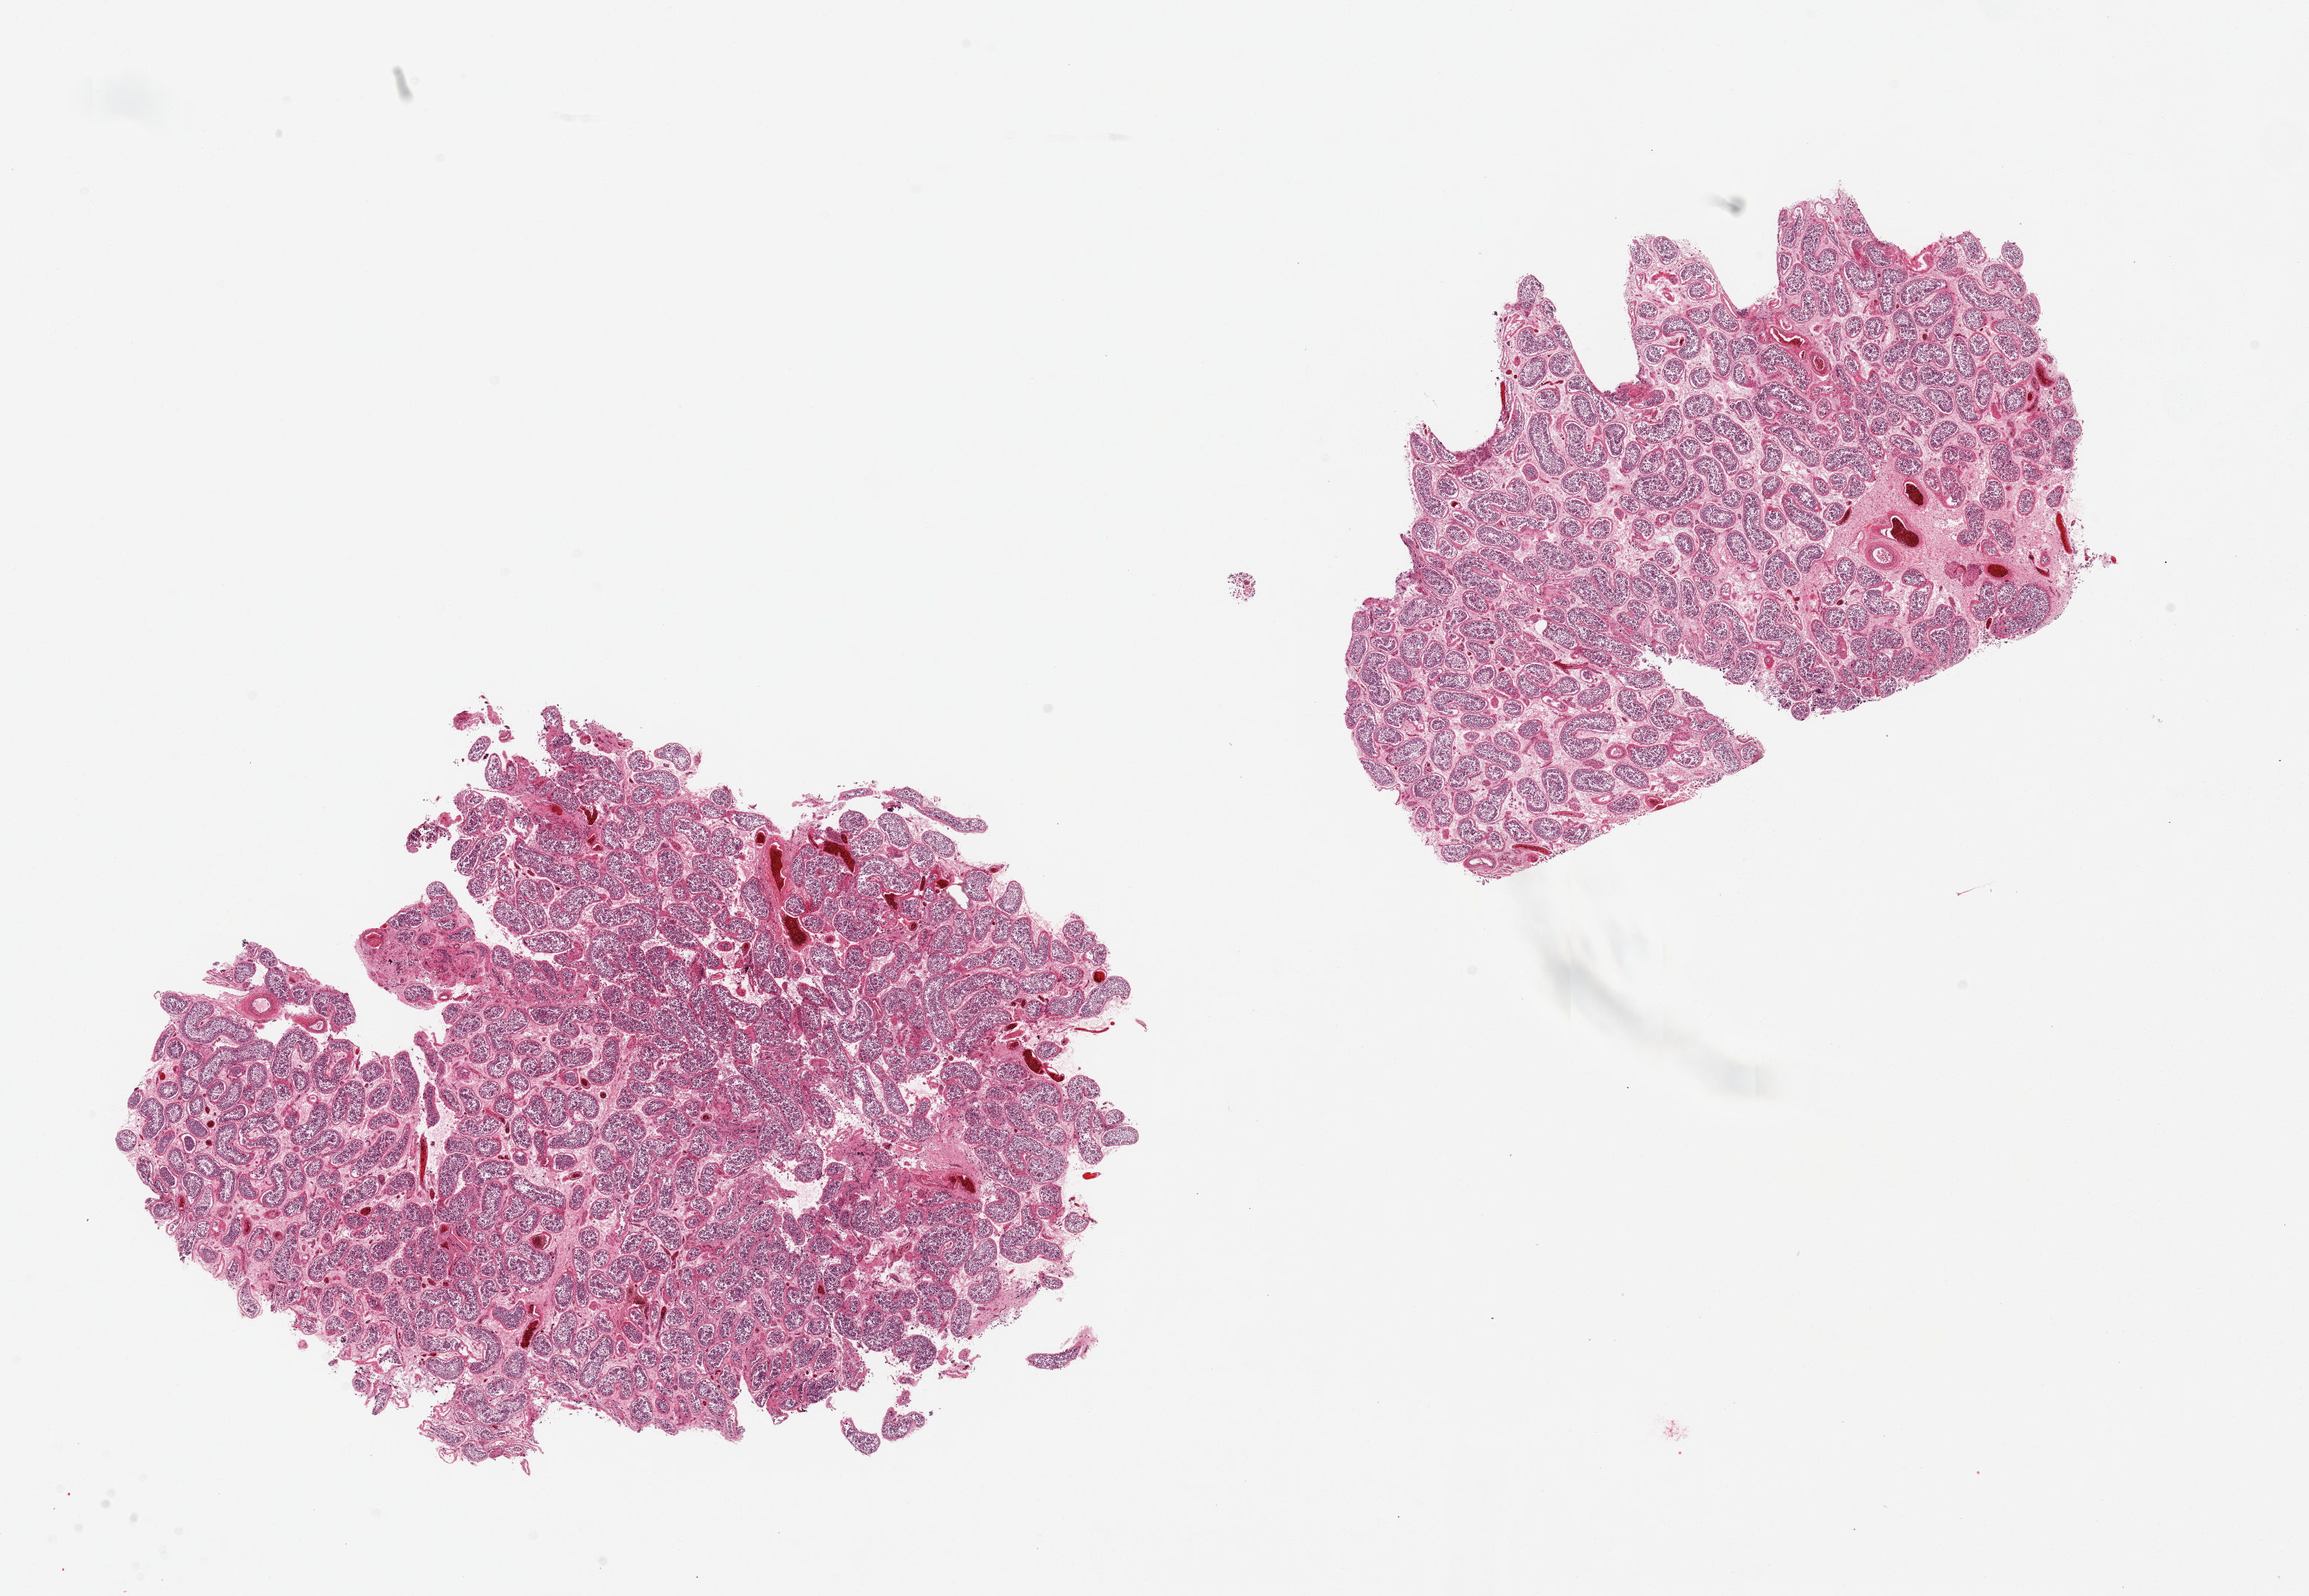
Whole-slide image, haematoxylin and eosin stain, brightfield, low-resolution overview of the scanned area, about 24.6 x 17.0 mm. PAXgene-fixed, paraffin-embedded tissue. Target tissue: testis. Donor tissue sample. Male donor.
Review note (as recorded): 2 pieces; spermatogenesis.